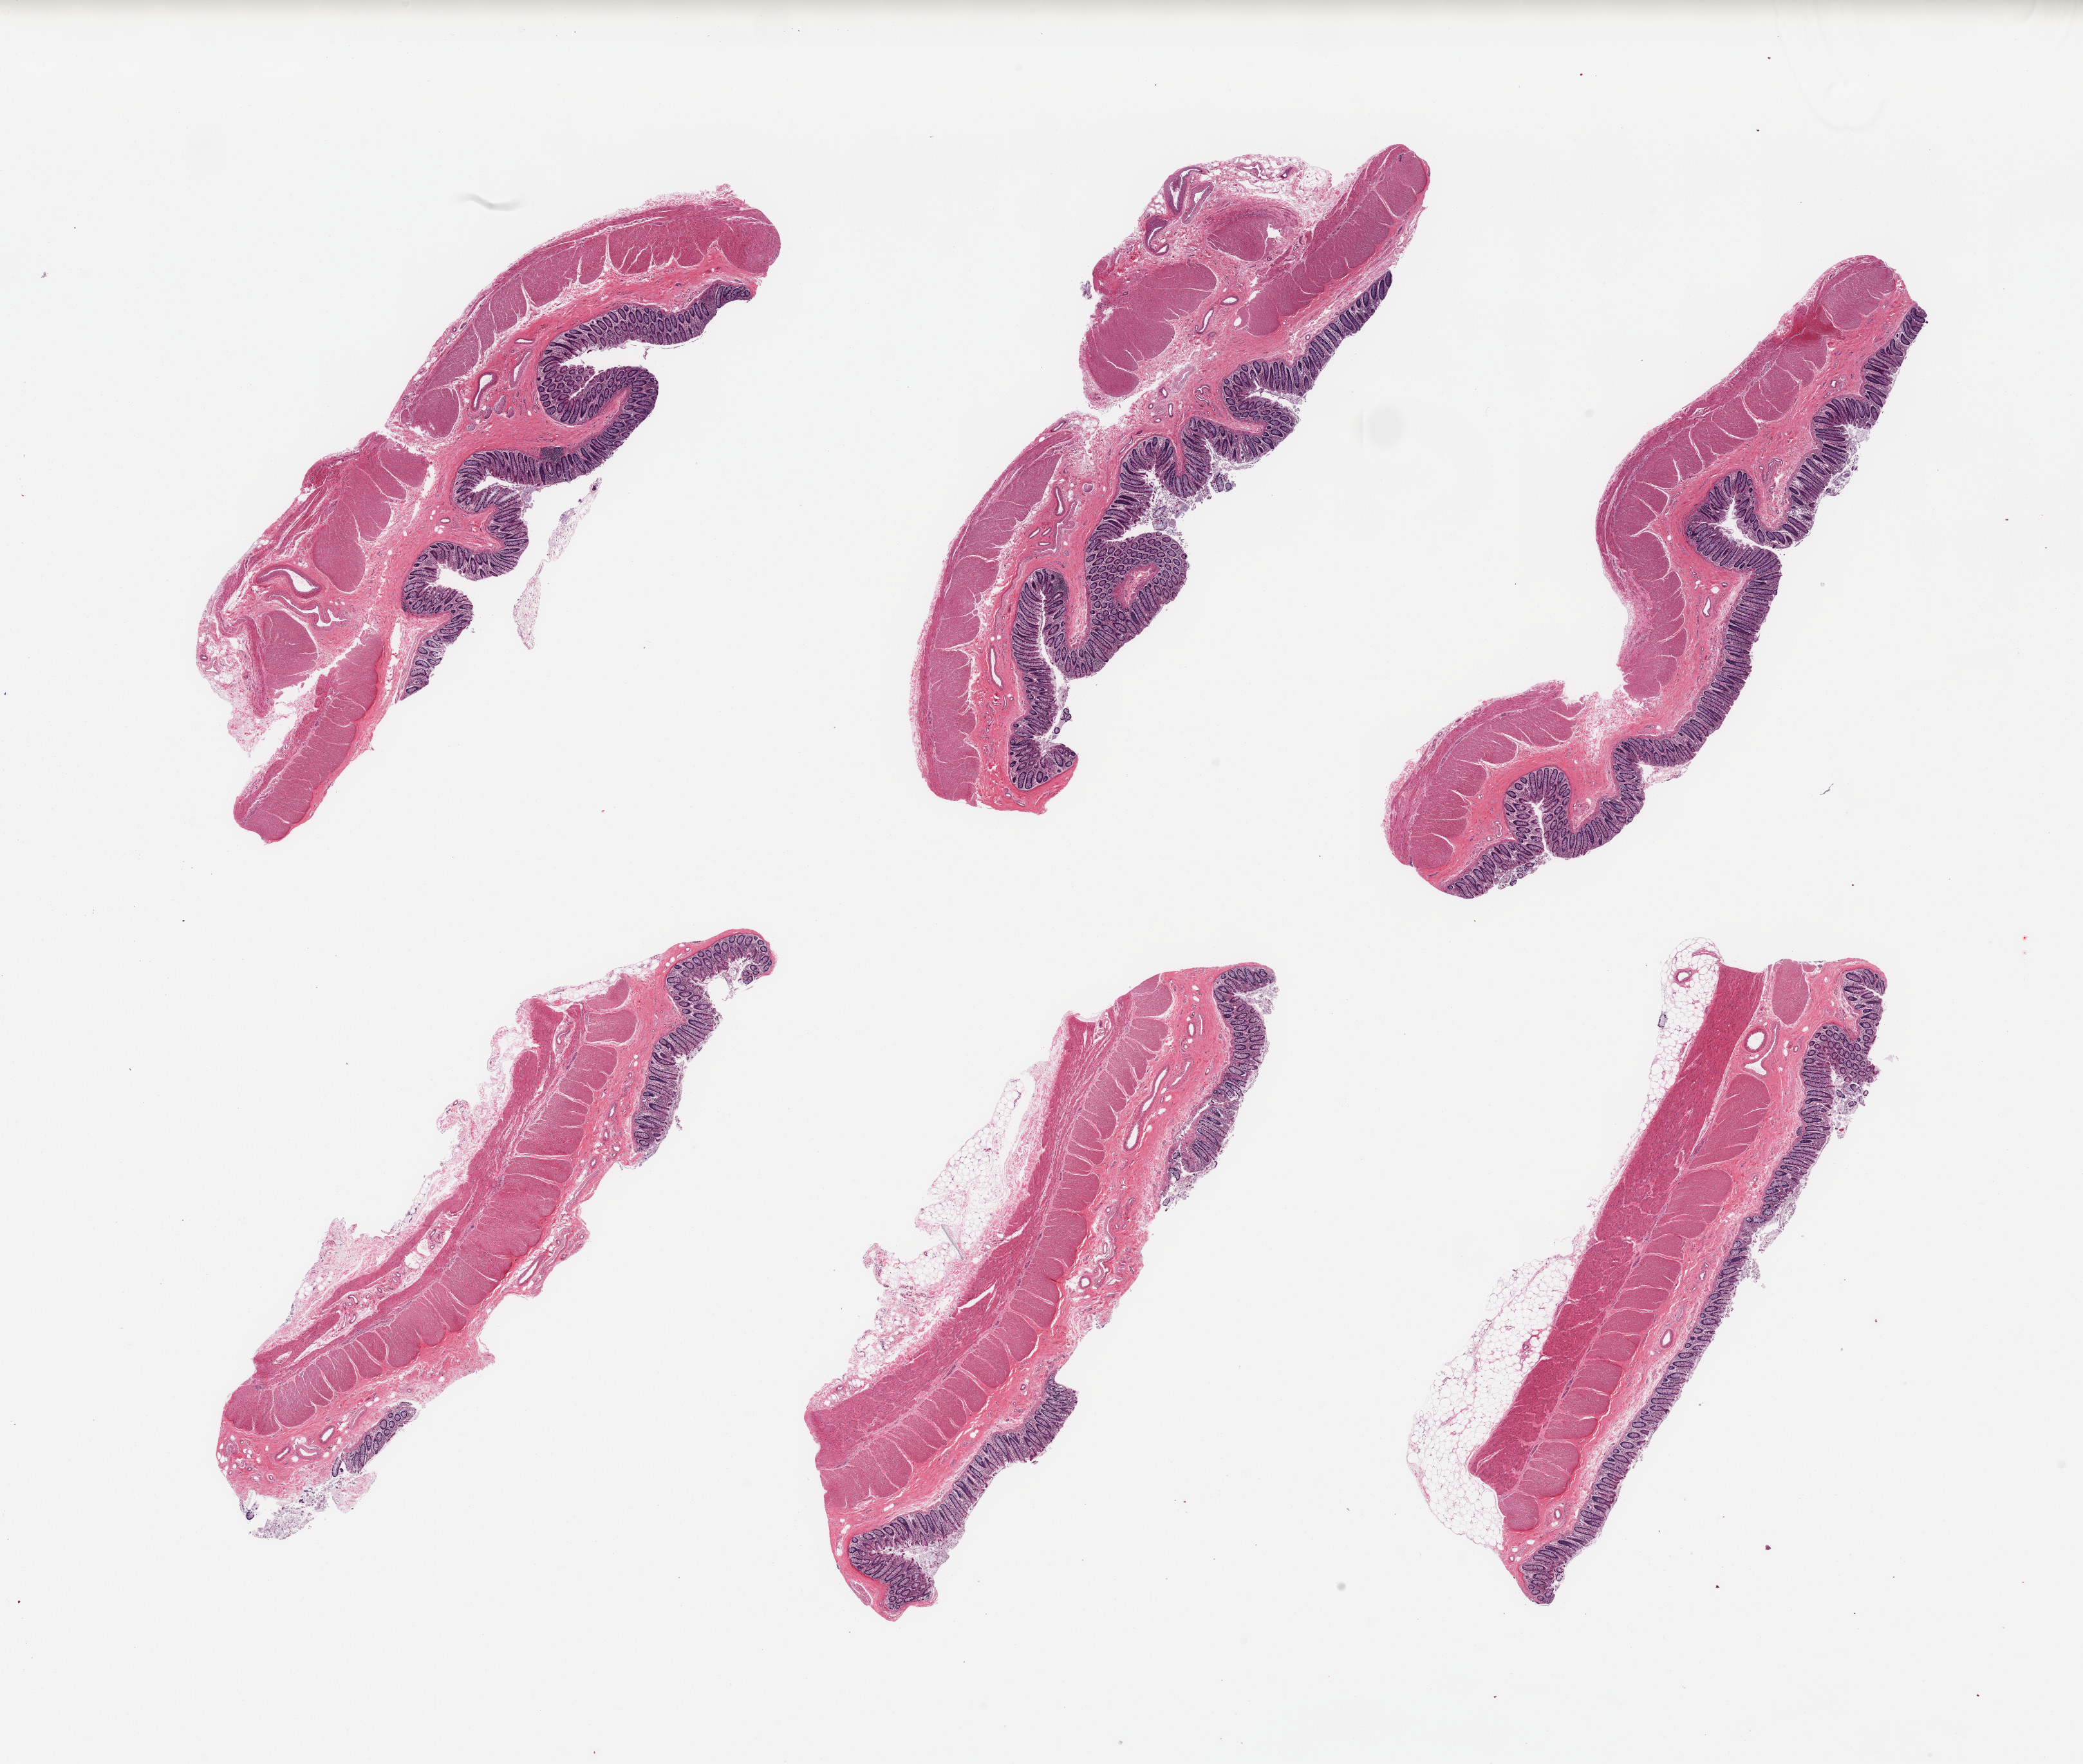
Digitized haematoxylin and eosin-stained section — a low-resolution overview of the entire scanned area, about 25.6 x 21.7 mm, PAXgene-fixed paraffin-embedded (PFPE) section, sampled site (target tissue): transverse colon, donor tissue sample. Donor sex: male.
* reviewer comment on this tissue sample: 6 pieces; well preserved mucosa & muscle